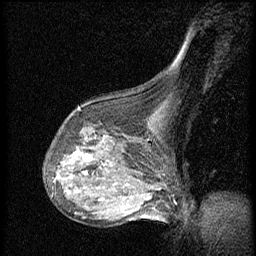
Breast MRI (dynamic contrast-enhanced), one sagittal slice. Position 41 of 56 along the scan axis. Dynamic contrast-enhanced series, image 2 of 3 at this slice position (ordered by acquisition). 1.5 T. TE 4.2 ms, TR 20.4 ms. 256 × 256 image matrix, field of view 200 × 200 mm. Female patient, age 64 years. Case-level facts recorded for this patient, not image findings: setting: breast cancer imaged before/during neoadjuvant chemotherapy; receptor status: HR-positive, HER2-negative.
Annotated regions visible in this slice (semi-automatically segmented with operator editing):
- analysis volume of interest (the breast-tissue region the enhancement analysis was run in; not a lesion): box from (x=48, y=104) to (x=142, y=186) px
- tumour enhancement mask (voxels above the 70 % enhancement threshold inside the analysis volume of interest): (x=73, y=153)–(x=80, y=156)